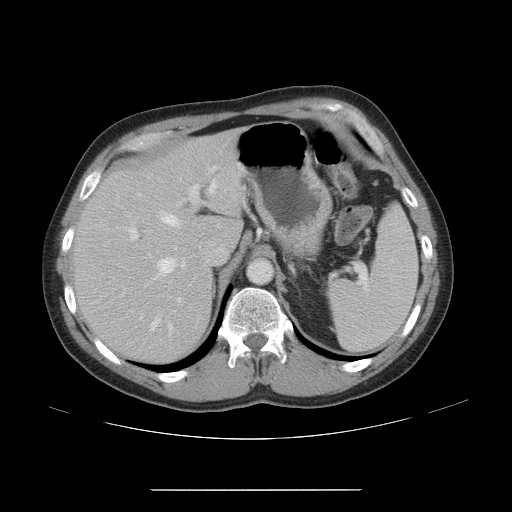
Contrast-enhanced abdominal CT, one axial slice. Slice 33 of 48 in the series (ordered by position). Intravenous contrast given. Soft-tissue window (W 400 / L 40 HU). 5 mm slice thickness. 512 × 512 image matrix. Male patient, age 56 years. From the clinical record (not read from this slice): diagnosis: colorectal cancer liver metastases, imaged before liver resection; multiple liver metastases: yes; largest metastasis: 1.8 cm; disease in both lobes: yes.
Outlined on this slice (expert manual segmentation):
- hepatic veins: box from (x=113, y=192) to (x=180, y=335) px
- liver: (x=77, y=134)–(x=242, y=361)
- planned liver remnant (the part of the liver to remain after resection): (x=78, y=134)–(x=242, y=361)
- portal vein (with intrahepatic branches): (x=126, y=165)–(x=220, y=303)